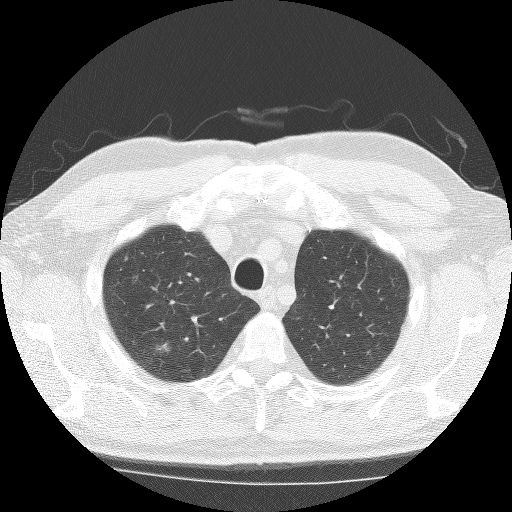
Chest CT (low-dose screening protocol), one axial image, first (baseline) screen, lung window (W 1500 / L -600 HU), 2.5 mm slice thickness, 120 kVp, slice 16 of 38 in the series, 512 × 512 image matrix, field of view 350 × 350 mm. Male participant, aged 74 years at enrolment.
Lesion marked by an expert reader, bounding box [x1, y1, x2, y2] px = [140, 331, 190, 370]. The screening reader recorded 3 non-calcified nodules or masses ≥4 mm on this exam (right upper lobe, right lower lobe, right middle lobe); which of them this box marks is not recorded. Official screen result: positive, change unspecified: nodule(s) >= 4 mm or enlarging nodule(s), mass(es), or other non-specific abnormalities suspicious for lung cancer. Lung cancer was diagnosed 140 days after this screen: bronchiolo-alveolar carcinoma, non-mucinous, right upper lobe, stage IA (AJCC 6th edition), 14 mm at pathology.